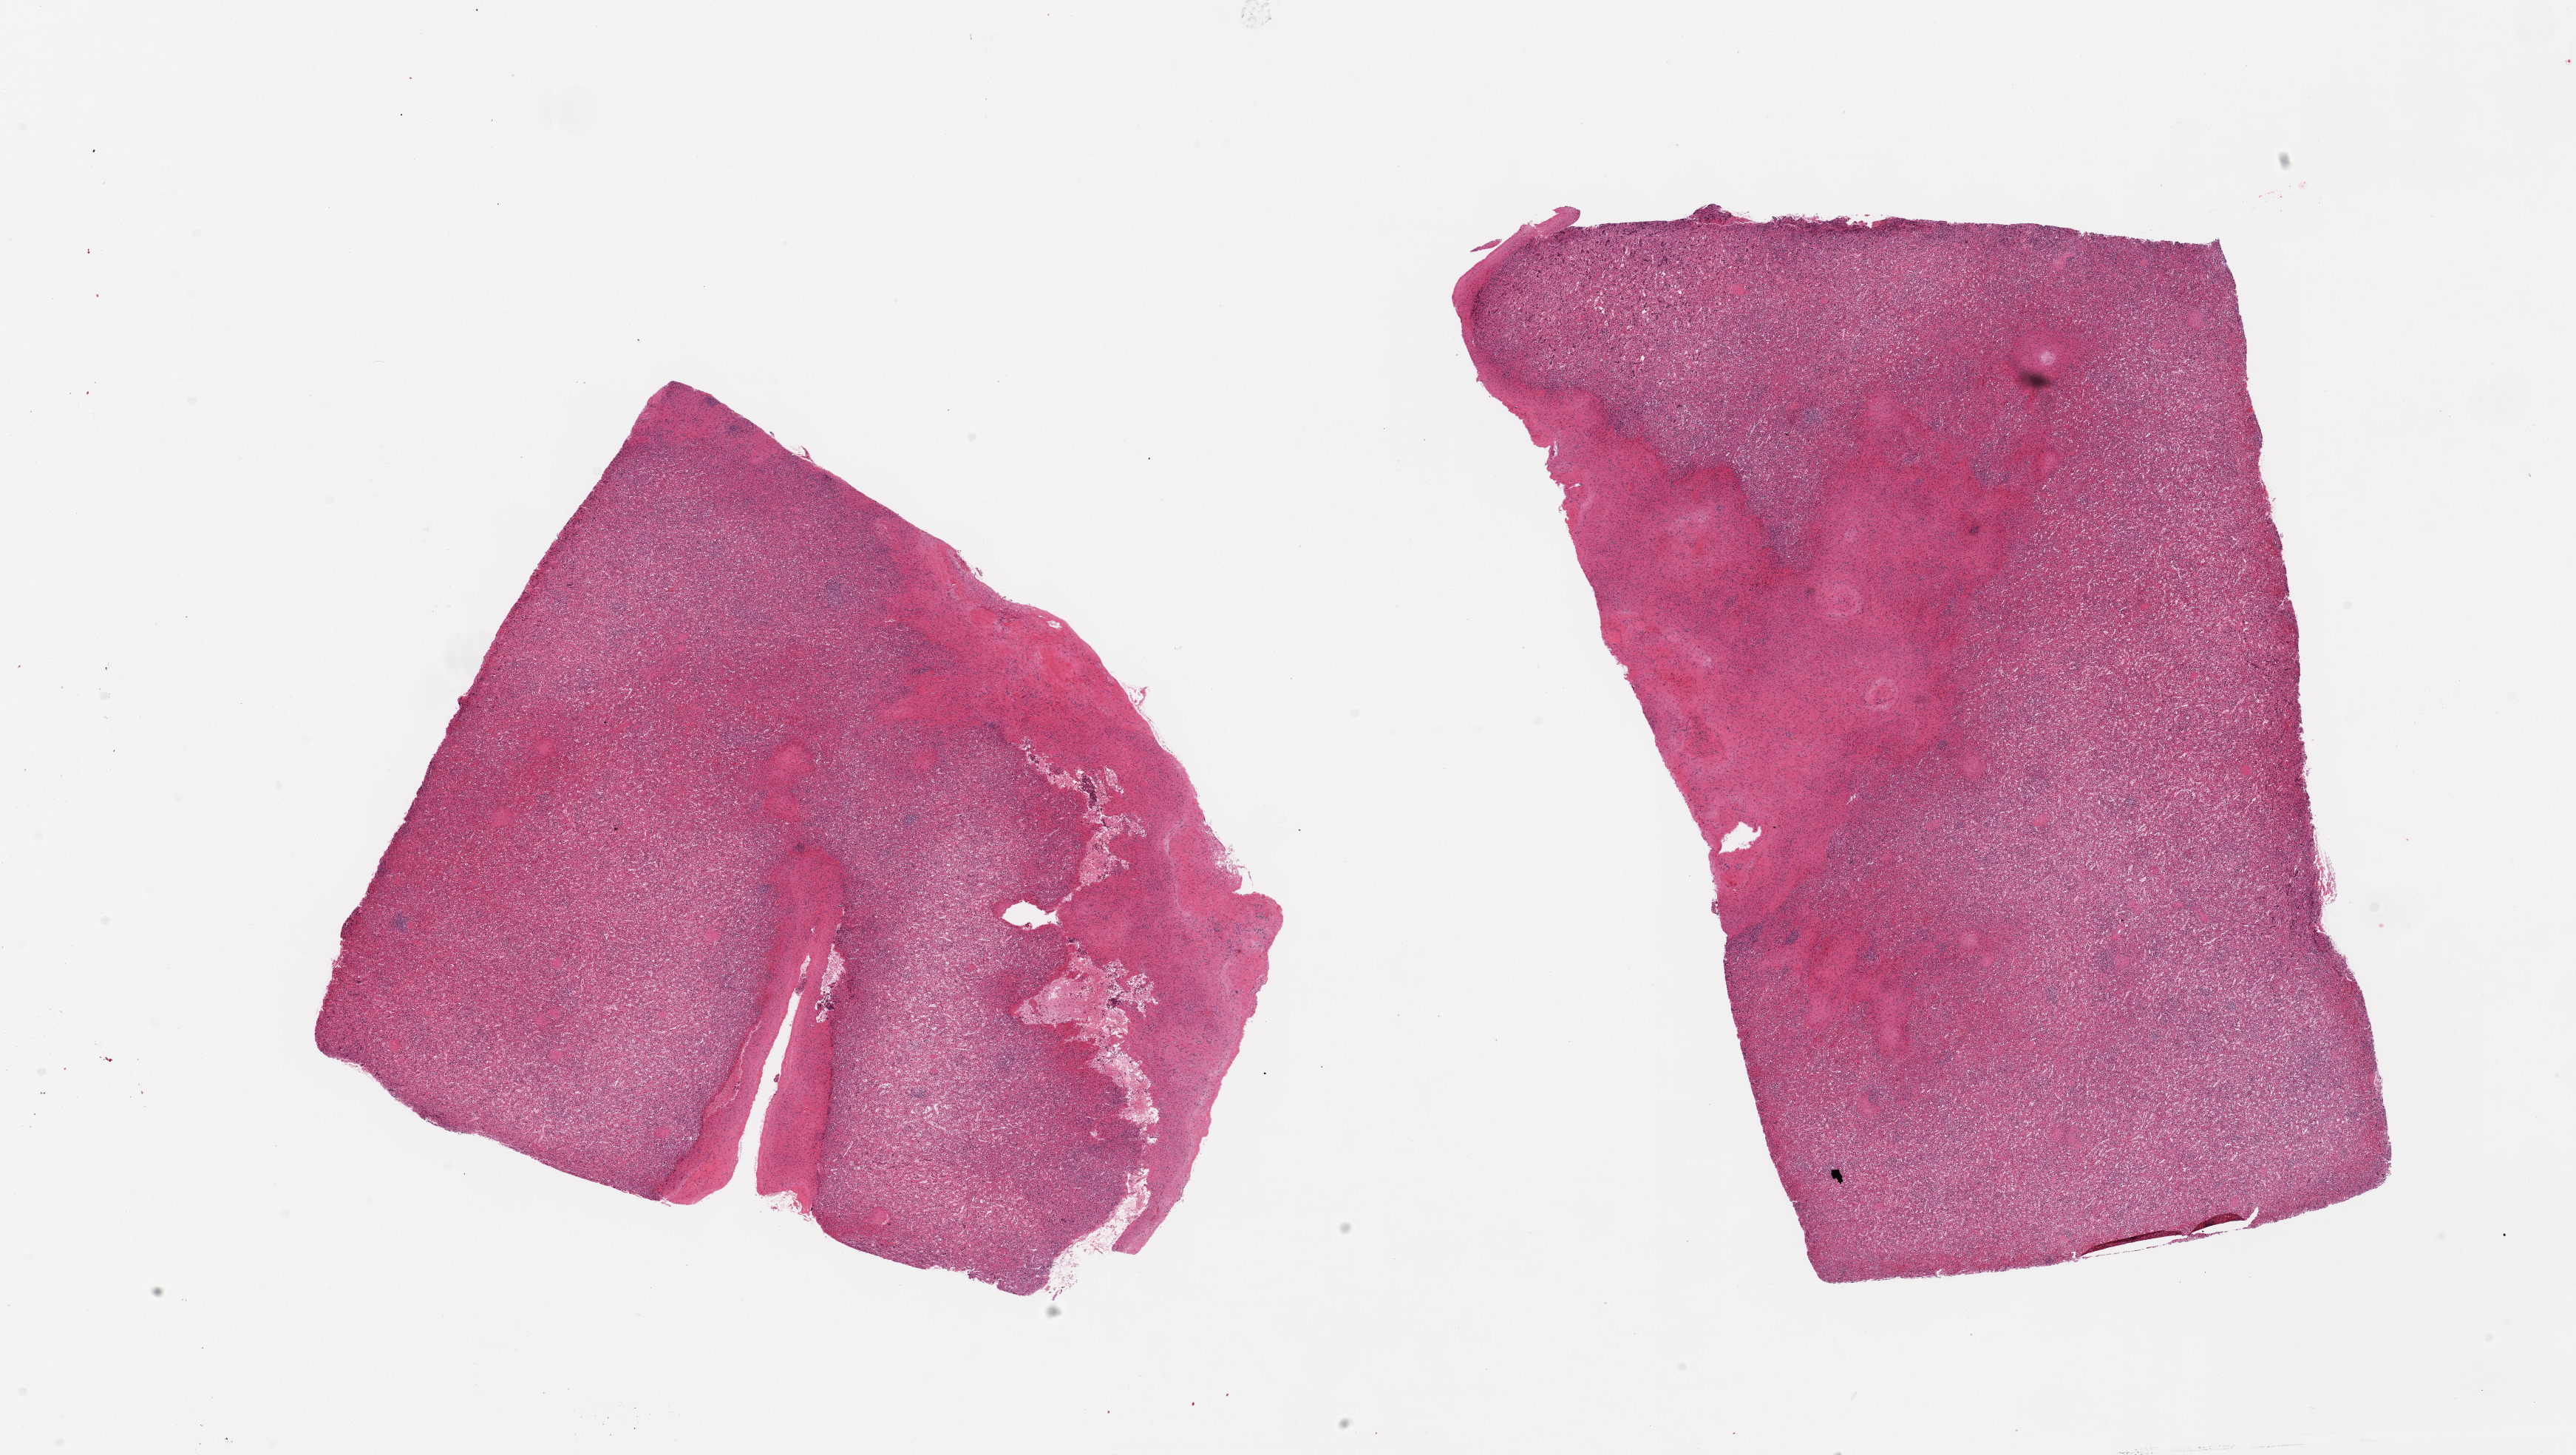
H&E whole-slide image, whole scanned area (about 27.6 x 15.6 mm, from a 20x scan) shown as a low-resolution overview, PAXgene-fixed paraffin-embedded (PFPE) section, section of spleen (target tissue), donor tissue sample. Male donor.
Reviewer comment on this tissue sample: 2 pieces; thick capsule included; congestion.